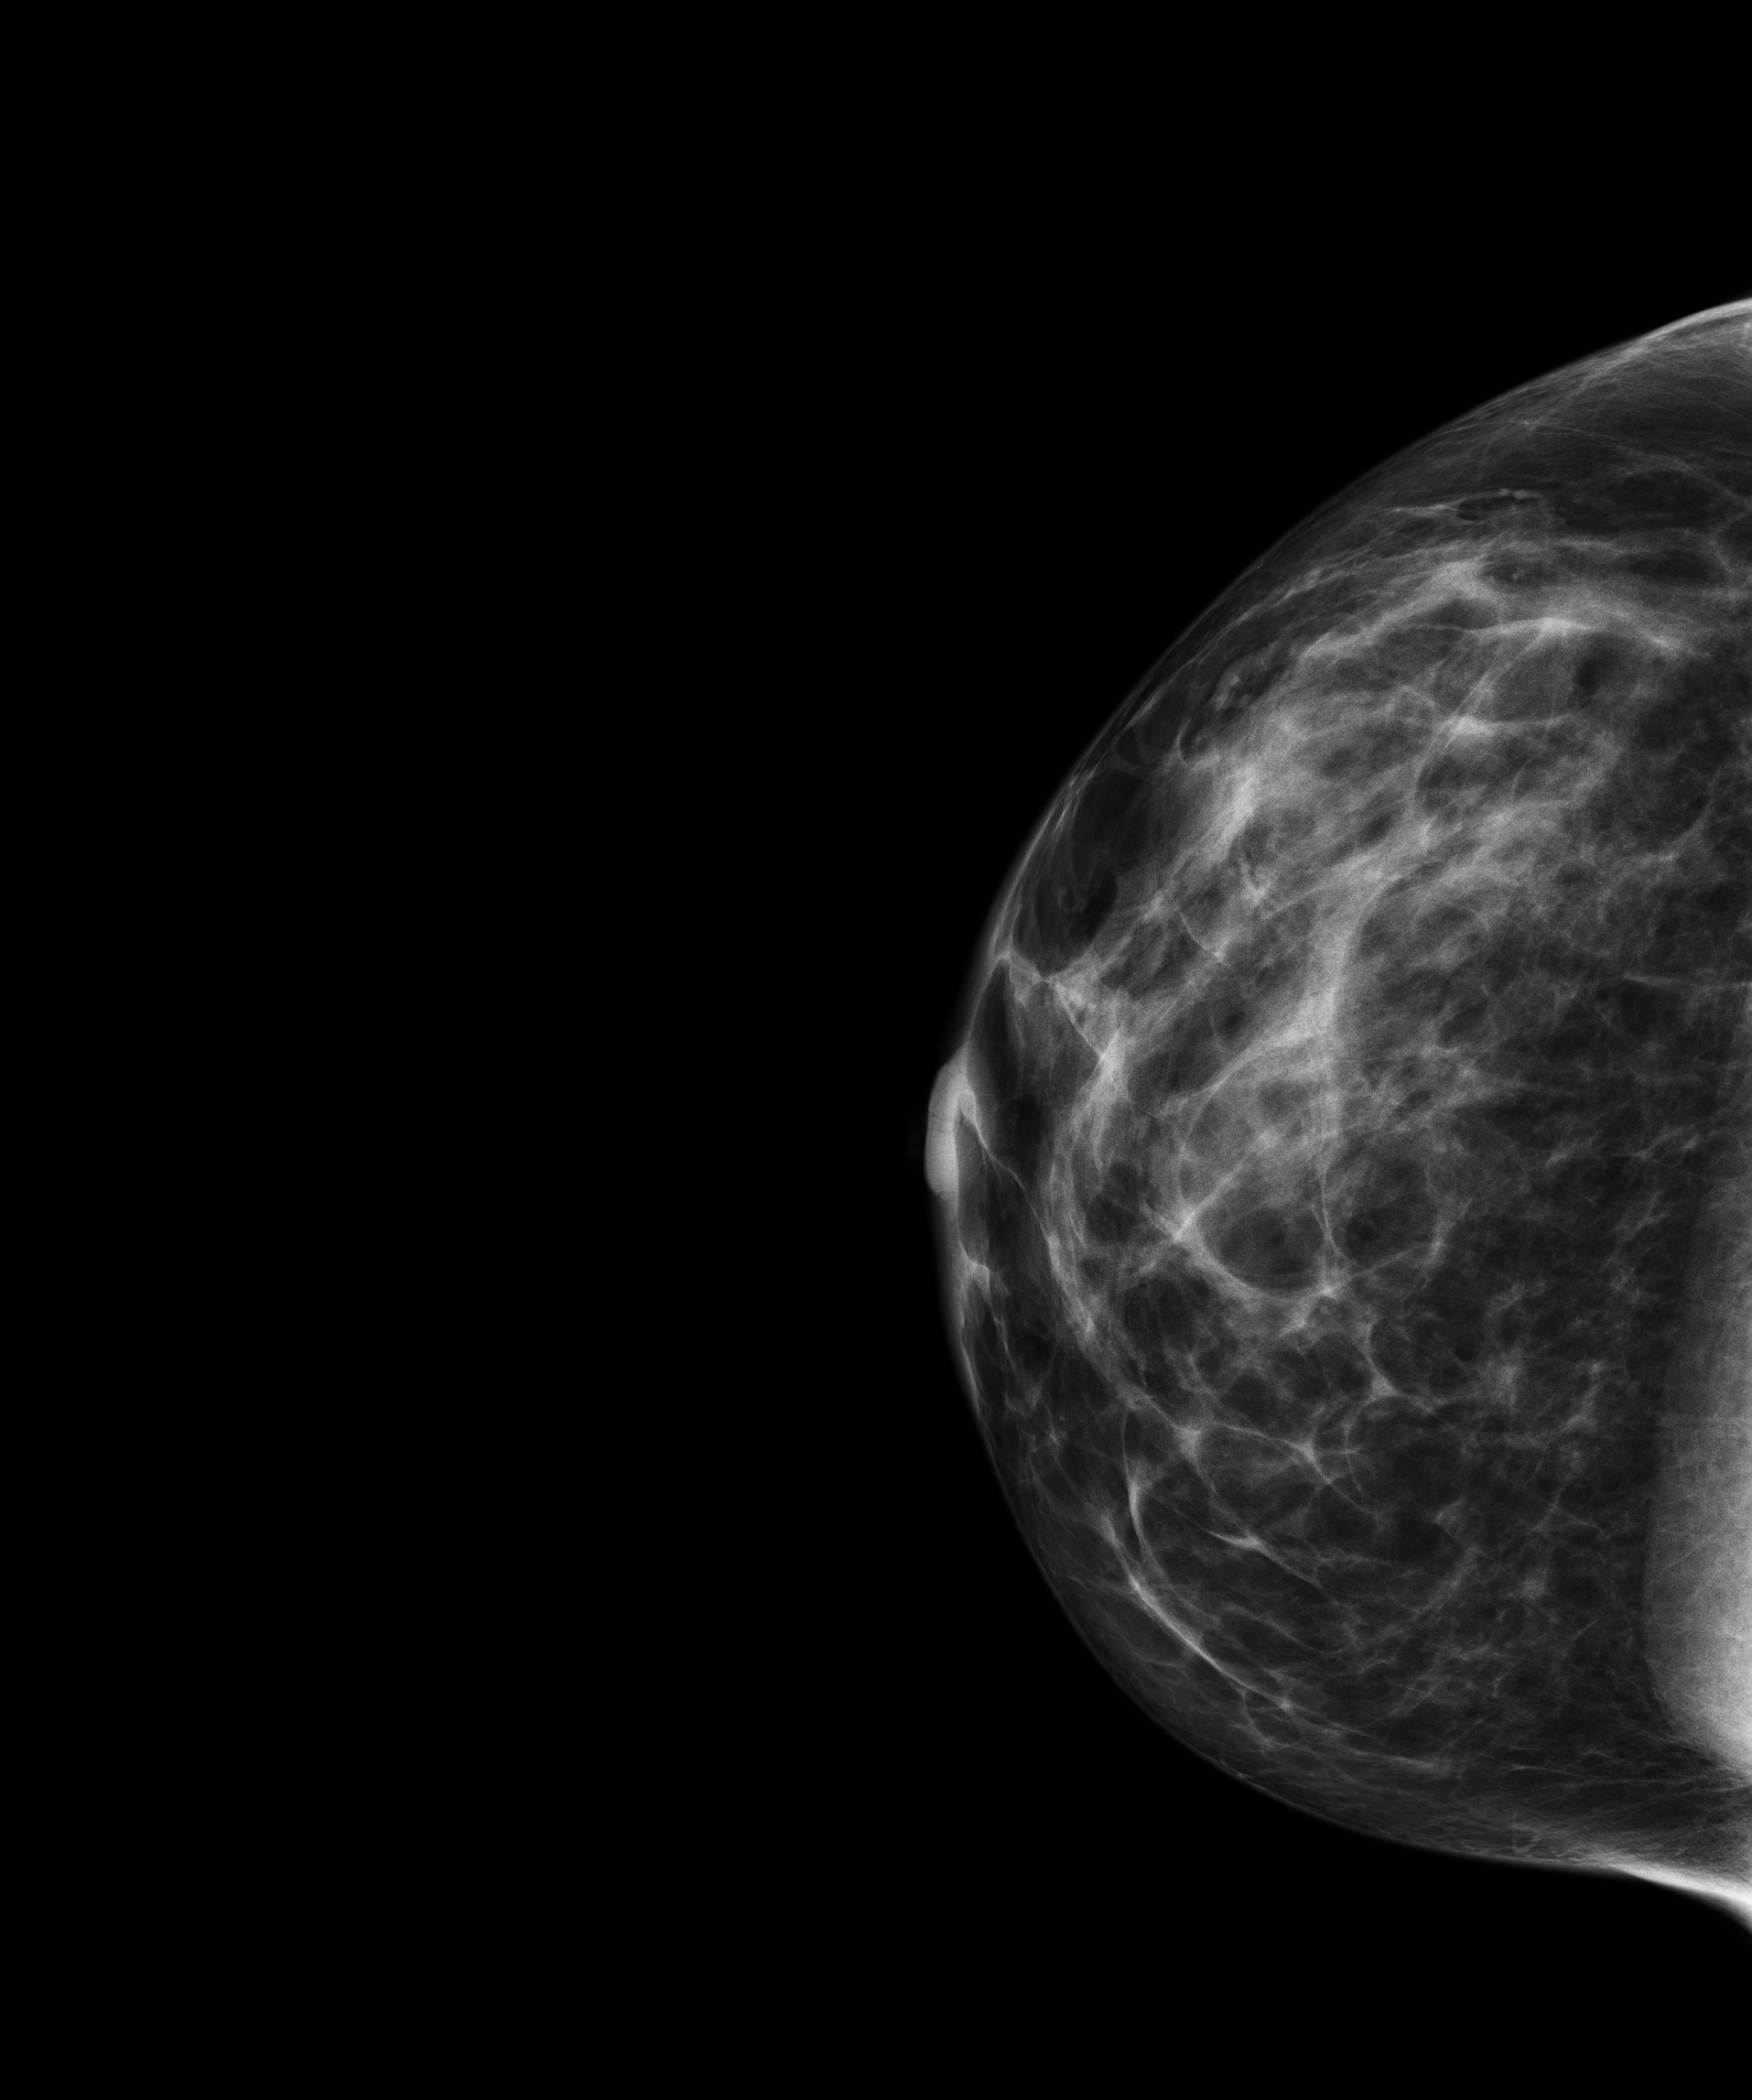
Full-field digital mammogram (FFDM), right breast, cranio-caudal projection, screening examination. Patient: female, 45 years.
BI-RADS breast density category at the screening exam (both breasts, scale 1–4): 3. Final BI-RADS category for the screening round (tomosynthesis exam, both breasts): category 1. Recall: no recall after this screen.